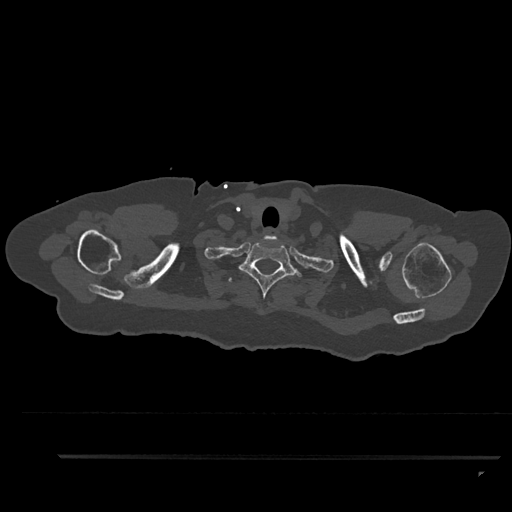
CT including the spine, one axial slice; slice 762 of 797 in the series (ordered by position); reconstruction kernel Br40s/3; 120 kVp; bone window (W 1800 / L 400 HU); 512 × 512 image matrix, field of view 408 × 408 mm. Female patient, age 44 years. From the clinical record (not read from this slice): primary cancer: renal.
Annotated regions visible in this slice (semi-automatically segmented with operator editing):
- T1 vertebra: bounding box [x1, y1, x2, y2] px = [238, 243, 309, 299]
- T2 vertebra: [229, 277, 232, 282]